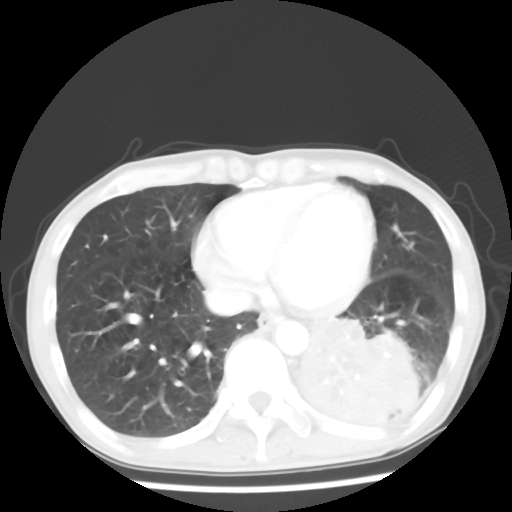
Chest CT, one axial slice; reconstruction kernel STANDARD; lung window (W 1500 / L -600 HU); 512 × 512 image matrix, field of view 313 × 313 mm. Patient: male, 68 years. From the clinical record (not read from this slice): clinical TNM (as recorded): T4 N0 M0.
Structures marked on this image (rectangle marked by the reading radiologist):
- lung tumour (recorded histology: squamous cell carcinoma): bounding box (x1, y1, x2, y2) in pixels: (281, 302, 431, 427)